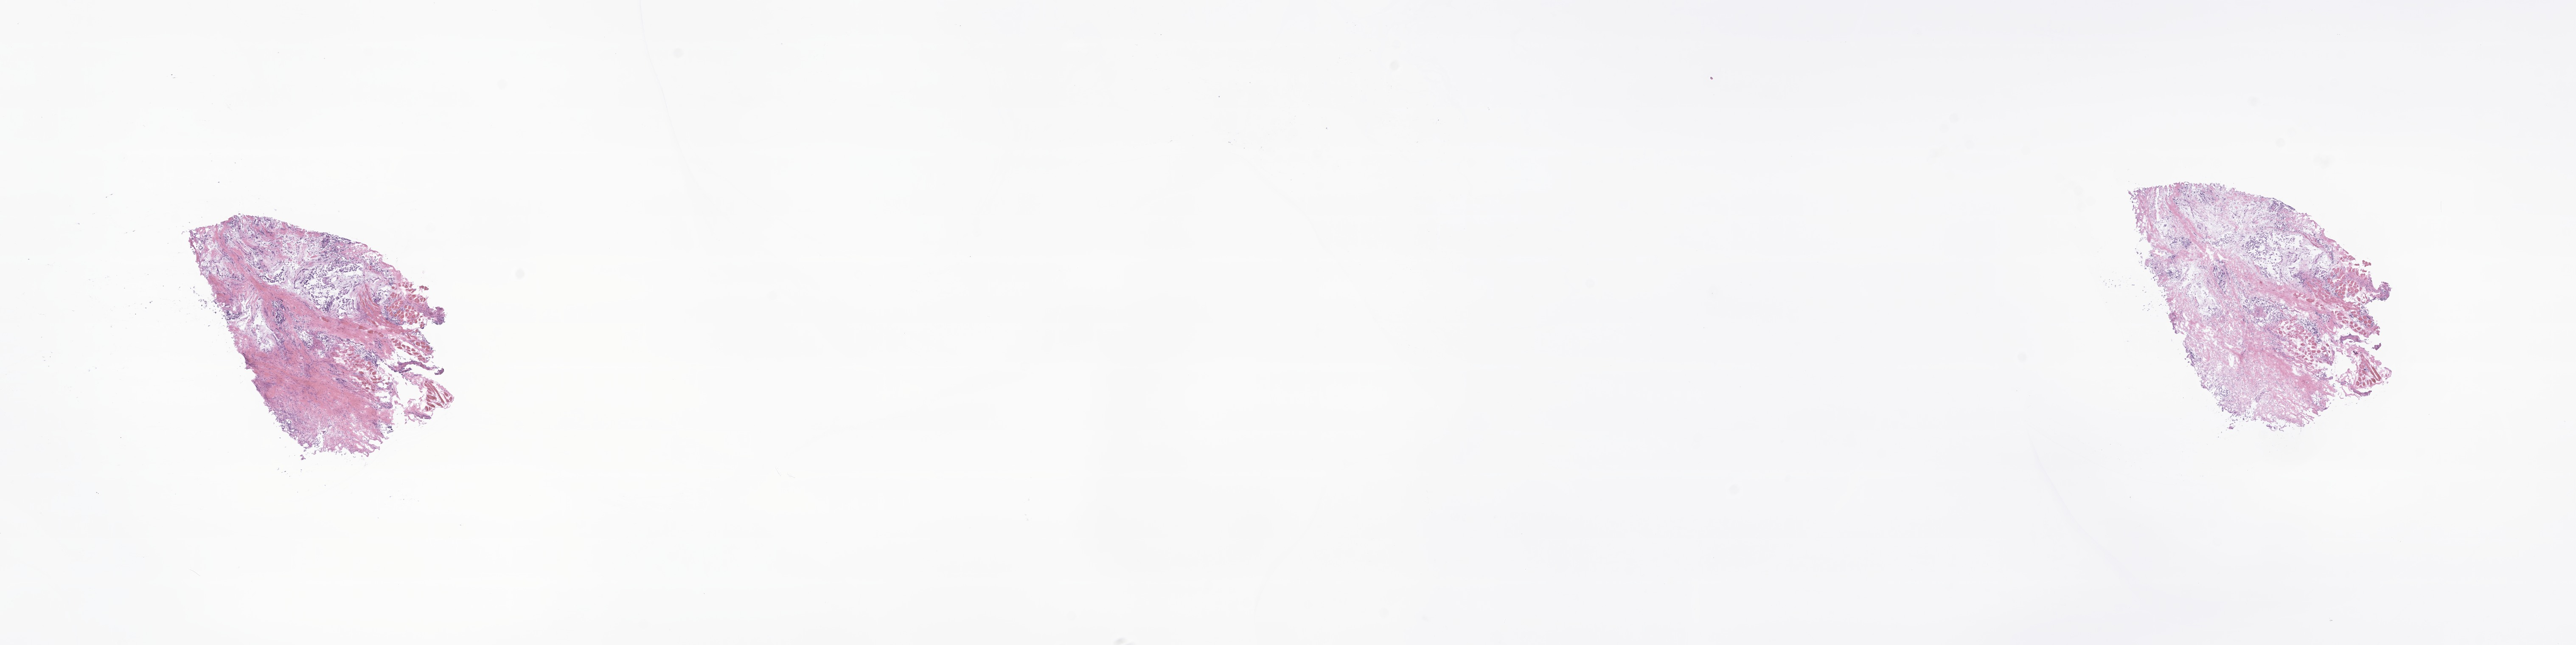
Whole-slide image, H&E stain of tumor tissue from the ethmoid sinus — low-resolution overview of the scanned area, about 25.6 x 6.4 mm; cryosection (OCT / tissue freezing medium). Patient: male, age 130 months (10 years 10 months).
• recorded diagnosis: Carcinoma, NOS